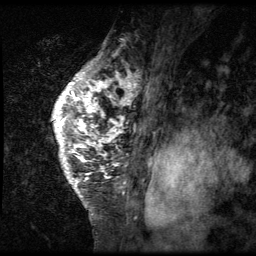
Breast MRI (dynamic contrast-enhanced), one sagittal slice; position 48 of 64 along the scan axis; 3 images stored at this slice position (order not interpretable as contrast timing); 1.5 T; TE 4.2 ms, TR 9 ms; 2.5 mm slice thickness; 256 × 256 image matrix, field of view 180 × 180 mm. Patient: female, 50 years. Case-level facts recorded for this patient, not image findings: setting: breast cancer imaged before/during neoadjuvant chemotherapy; receptor status: triple-negative.
Outlined on this slice (semi-automatically segmented with operator editing):
- analysis volume of interest (the breast-tissue region the enhancement analysis was run in; not a lesion): box from (x=33, y=39) to (x=138, y=212) px
- tumour enhancement mask (voxels above the 140 % enhancement threshold inside the analysis volume of interest): (x=51, y=53)–(x=138, y=186)